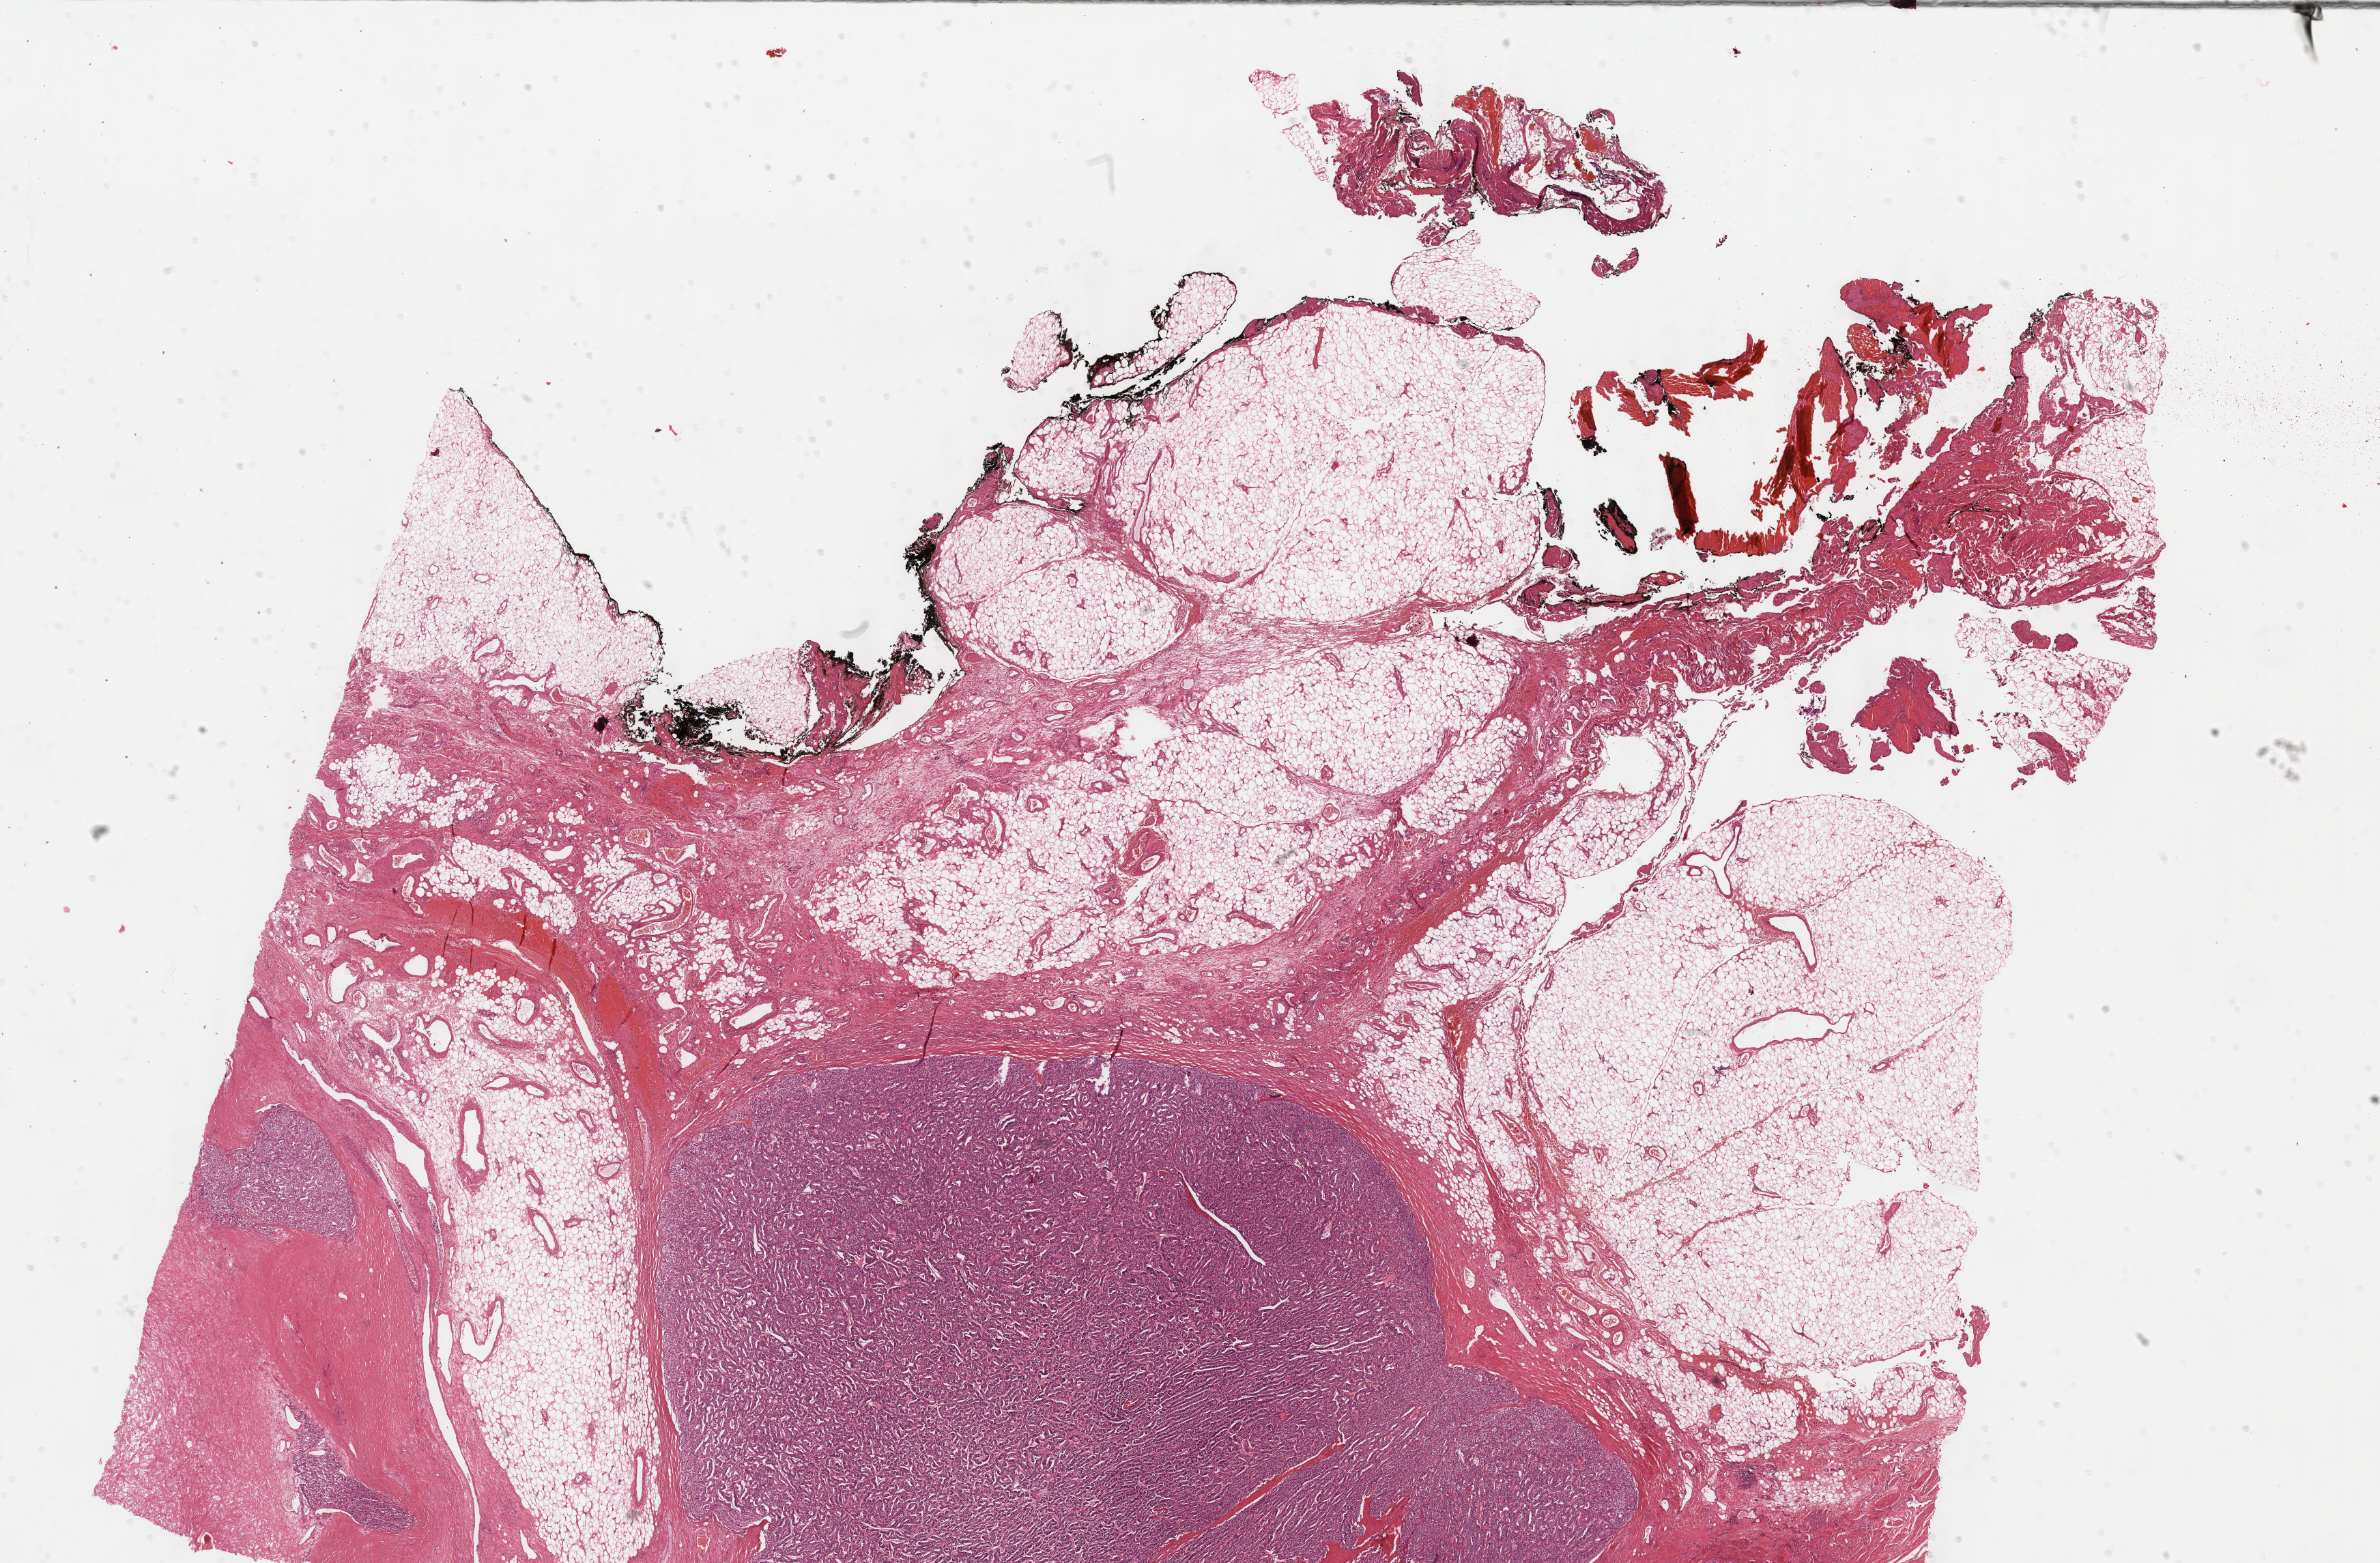
Whole-slide histology image, Hematoxylin and eosin (H&E) stained — a low-resolution overview of the entire scanned area, about 27.7 x 18.2 mm. Formalin-fixed paraffin-embedded (FFPE) diagnostic section. Sample: primary tumour, pancreas. Male, age 52 years at initial diagnosis. Histologic grade: G1 (well differentiated).
Lymph nodes positive (case pathology): 16 of 57 examined. Histologic diagnosis: Neuroendocrine carcinoma, NOS (head of pancreas). AJCC pathologic stage: IIB.